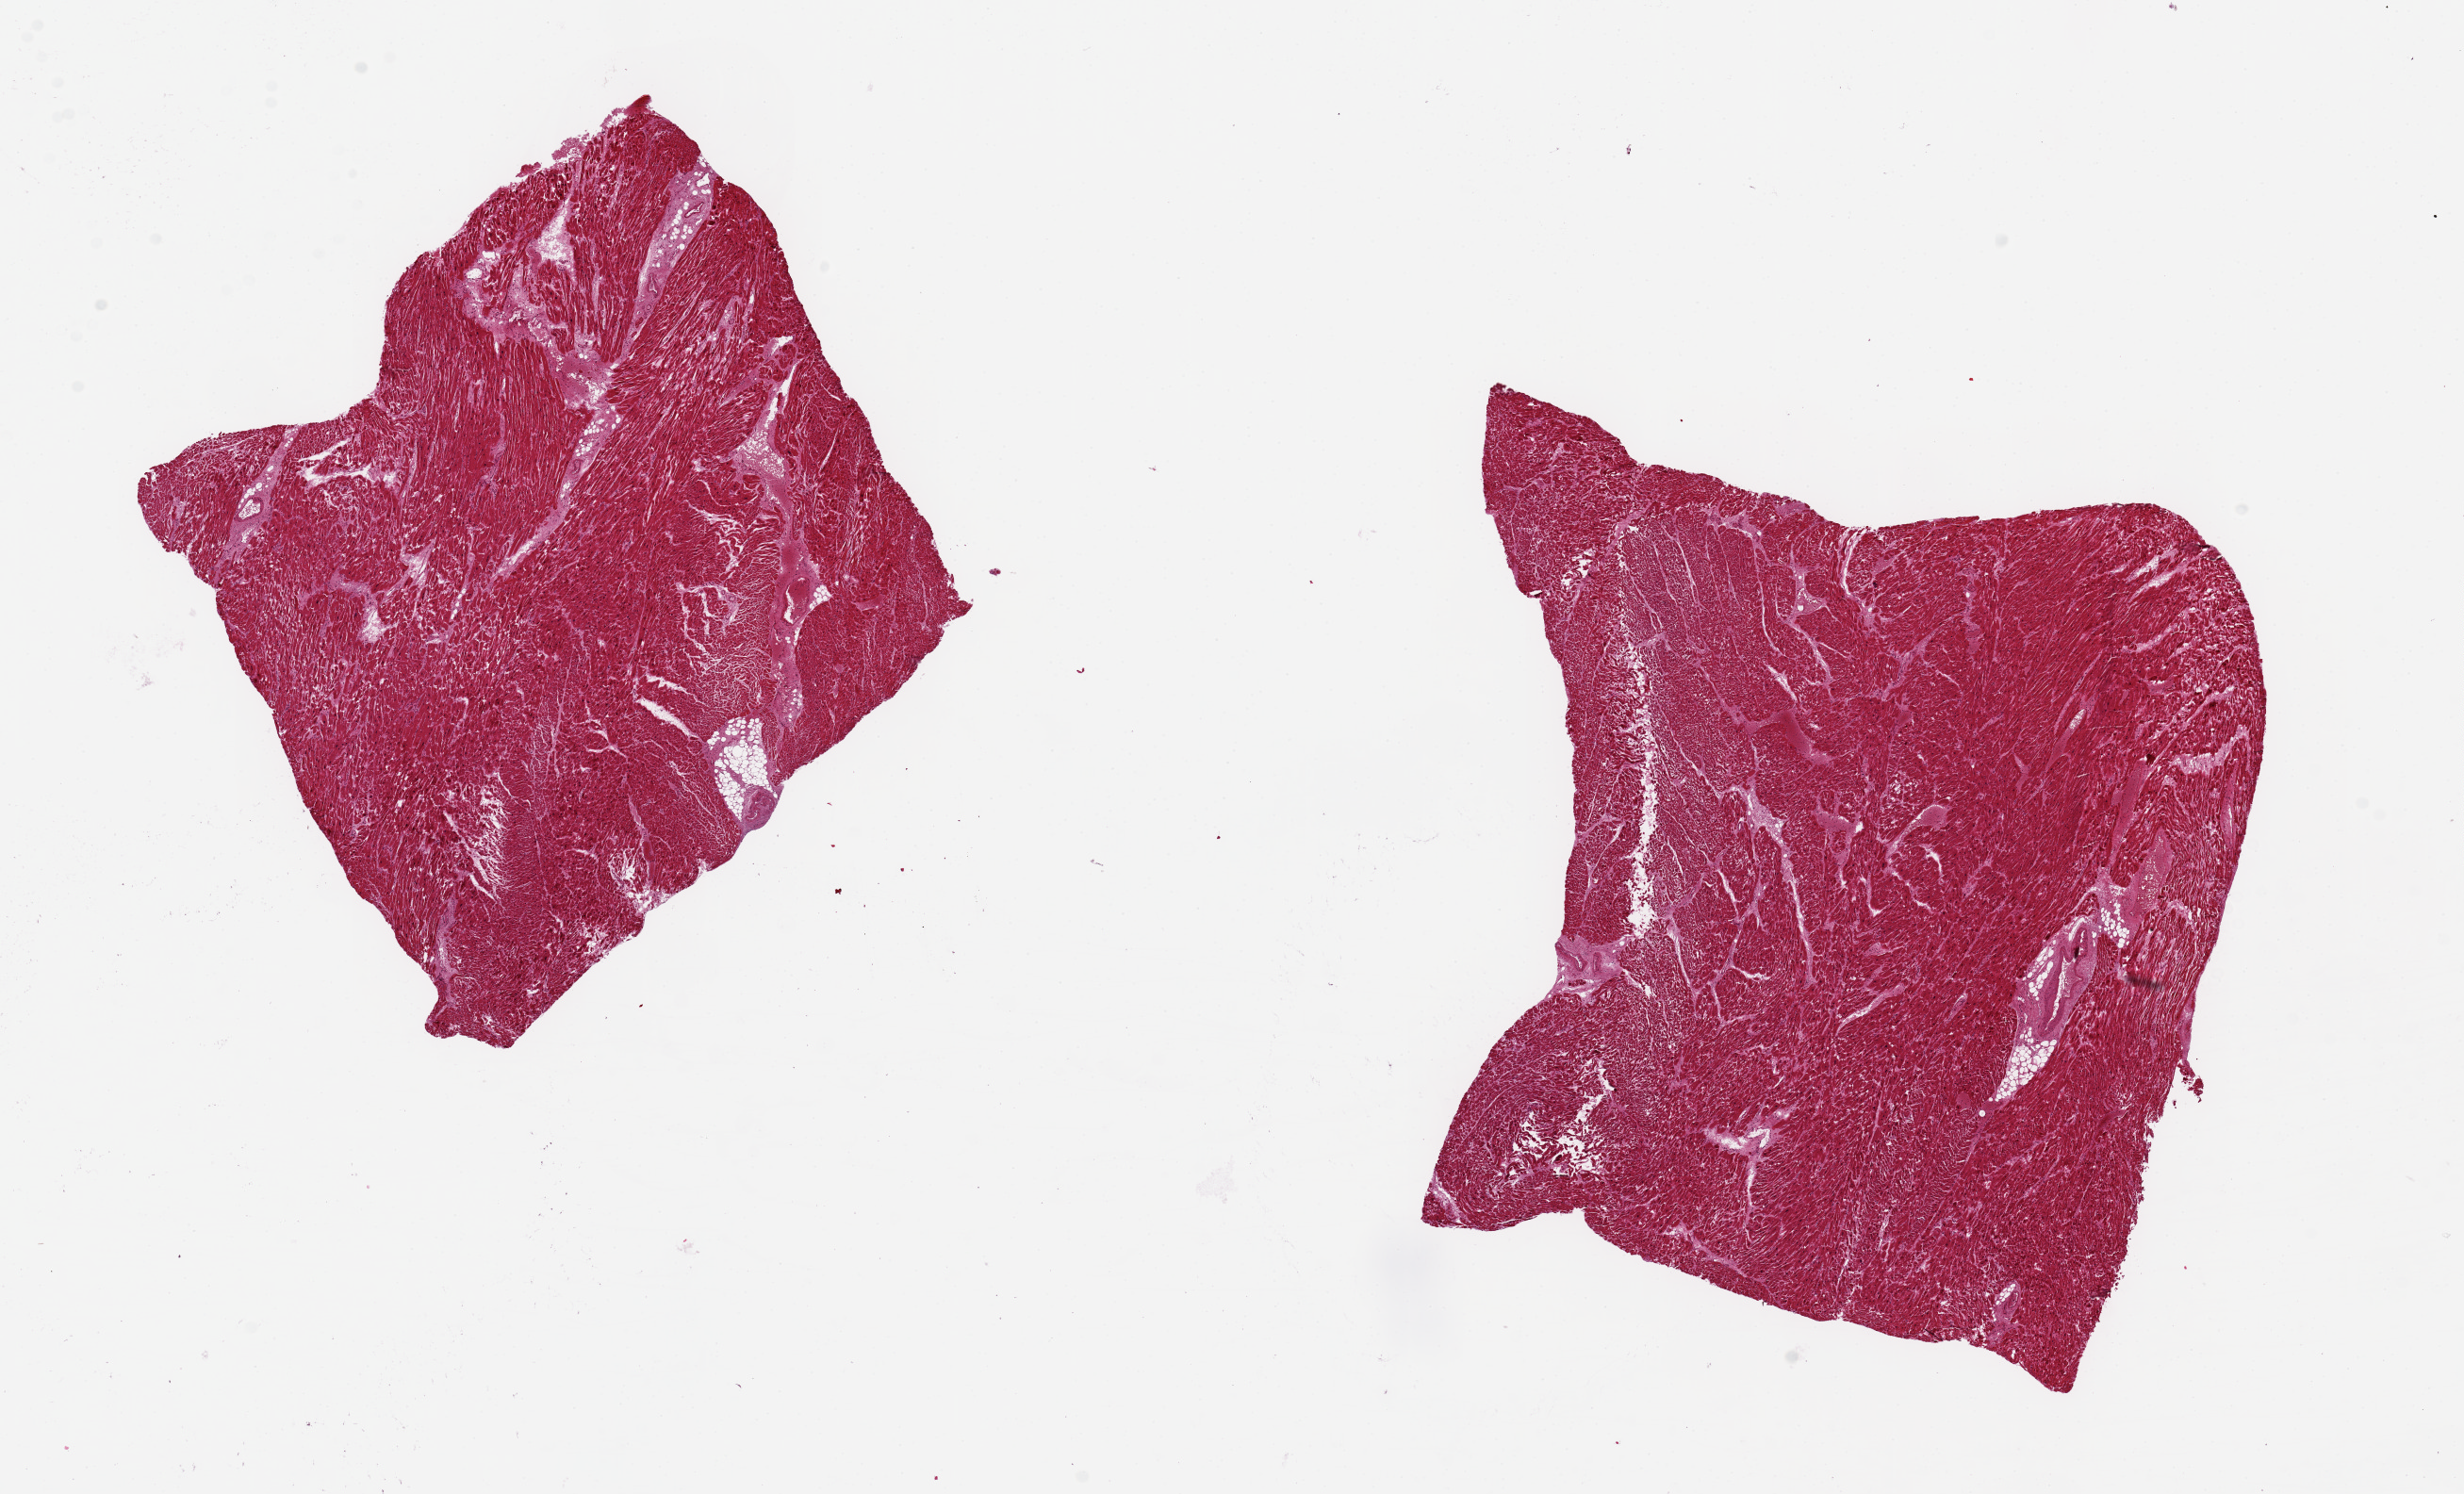
Digitized H&E-stained section — low-resolution overview of the scanned area, about 20.7 x 12.5 mm (acquisition: 20x scan); PAXgene-fixed paraffin-embedded (PFPE) section; target tissue: heart; tissue donor sample. Male donor.
* reviewer comment on this tissue sample: 2 pieces ~7x6mm Mildinterstital fibrosis, ischemic changes noted